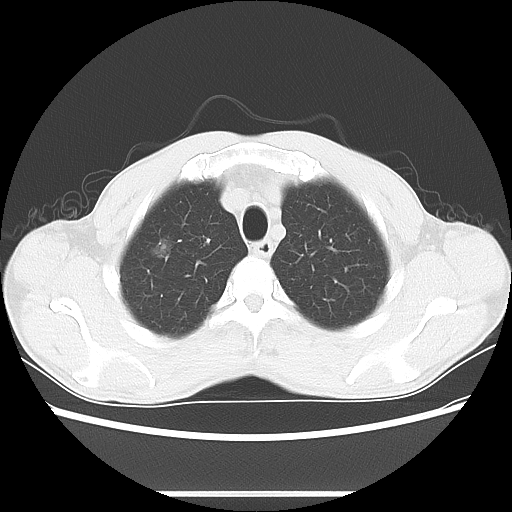
Chest CT, one axial slice; position 63 of 76 along the scan axis; lung window (W 1500 / L -600 HU); 512 × 512 image matrix. Male patient, age 54 years. Case-level facts recorded for this patient, not image findings: clinical TNM (as recorded): T1a N0 M0.
Annotated regions visible in this slice (rectangle marked by the reading radiologist):
- lung tumour (recorded histology: adenocarcinoma): bounding box (x1, y1, x2, y2) in pixels: (149, 229, 180, 266)